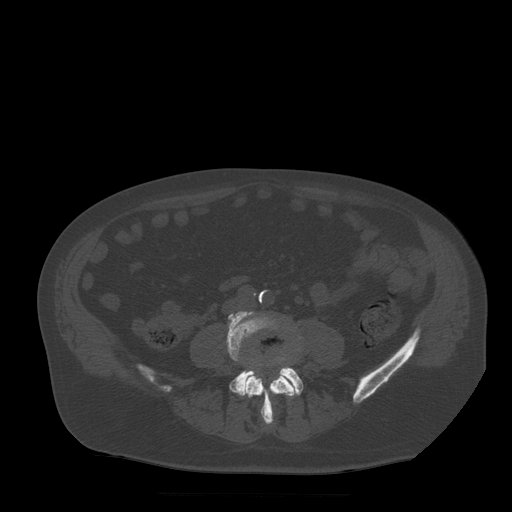
CT including the spine, one axial slice; slice 104 of 522 in the series (ordered by position); bone window (W 1800 / L 400 HU); 512 × 512 image matrix. Patient age 72 years. Case-level facts recorded for this patient, not image findings: primary cancer: prostate.
Annotated regions visible in this slice (semi-automatically segmented with operator editing):
- L4 vertebra: bounding box <227,312,296,425> (left, top, right, bottom; pixels)
- L5 vertebra: <230,358,304,398>